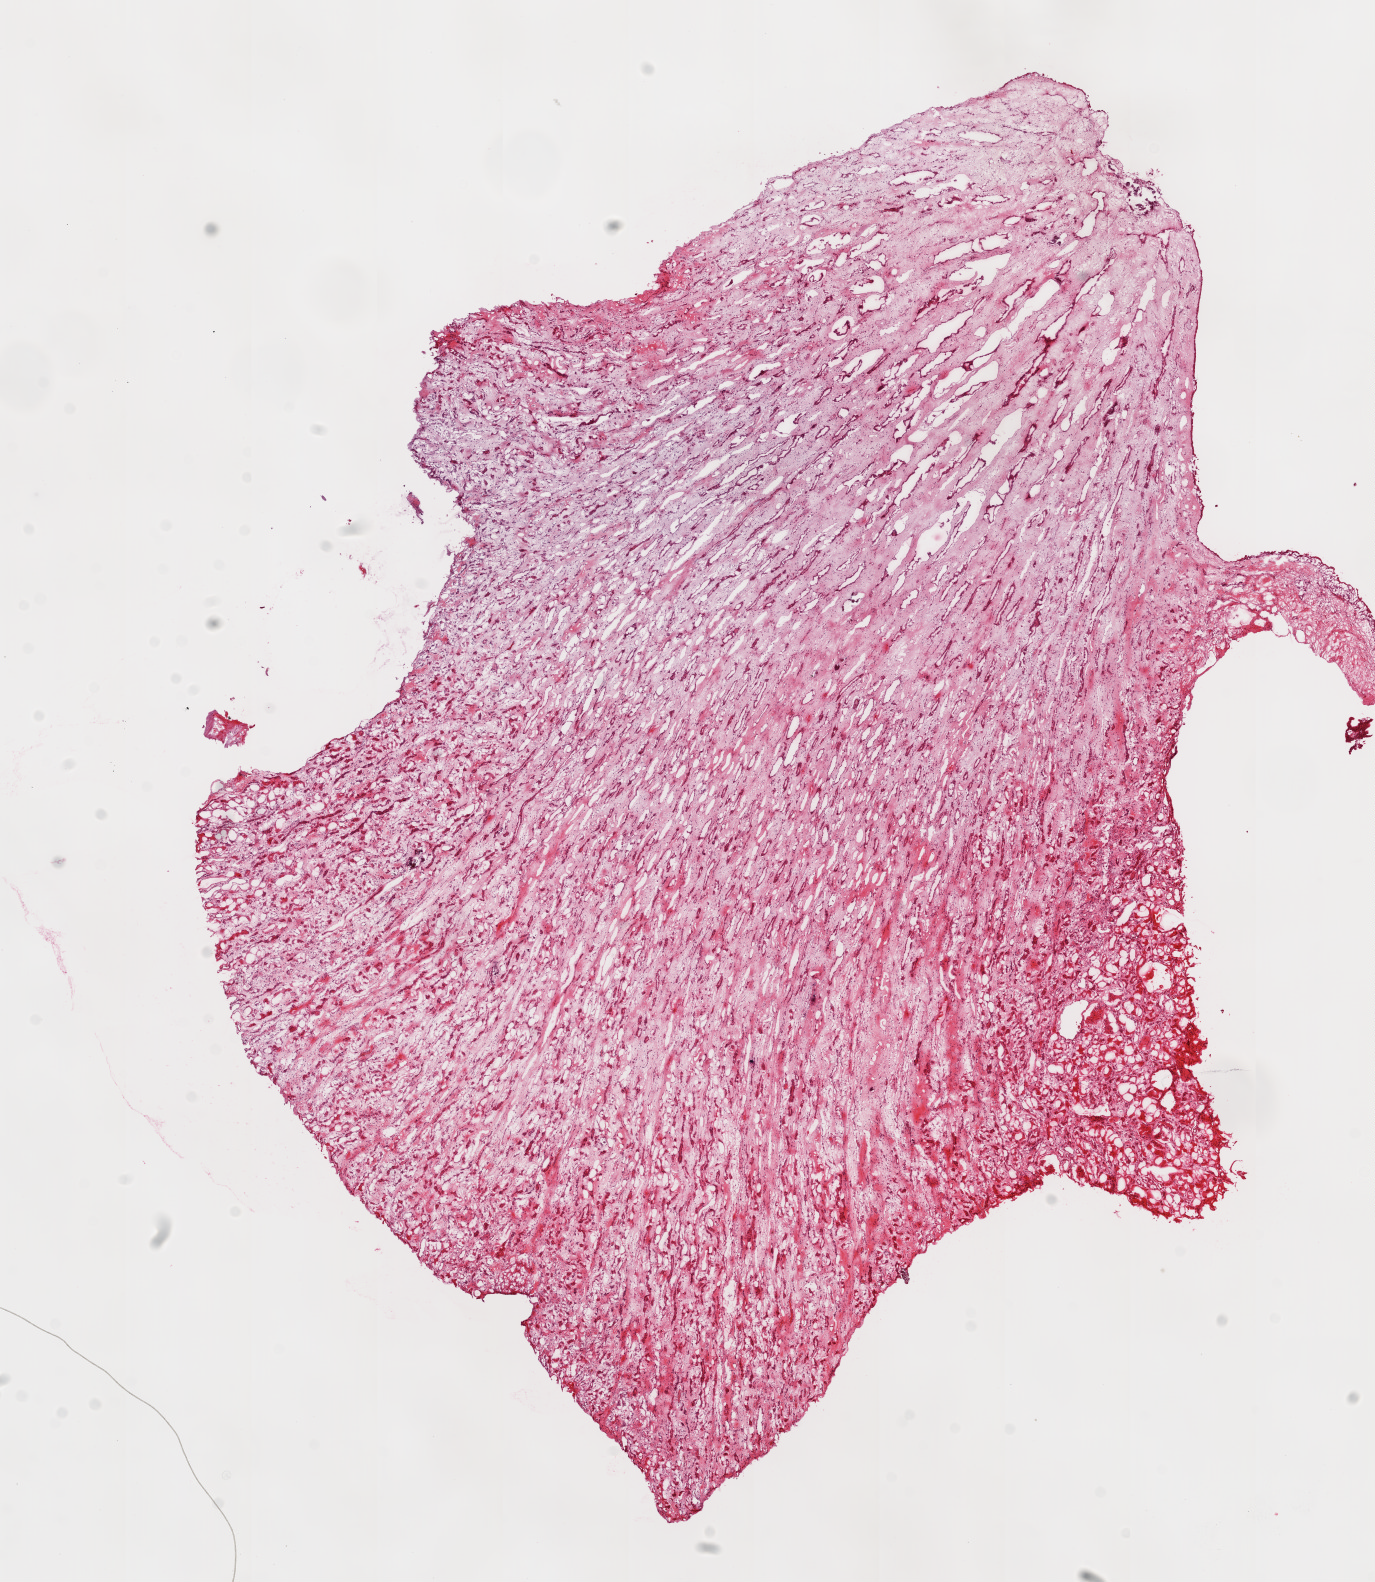
Whole-slide histology image, H&E-stained, whole scanned area (about 11.0 x 12.7 mm, acquisition: 20x scan) shown as a low-resolution overview, frozen section from the top of the tissue portion, kidney, solid tissue normal (non-tumour tissue) sample. Male, age 83 years at initial diagnosis.
This section: solid tissue normal (non-tumour) sample from the same patient. Patient diagnosis: Clear cell adenocarcinoma, NOS.